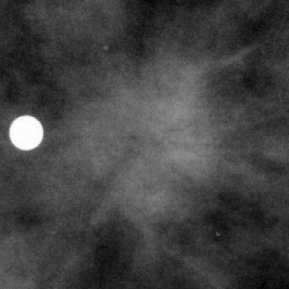
Region of interest cut from a scanned film mammogram (one marked finding); right breast; CC view.
Marked abnormality: calcifications, morphology round and regular / punctate, distribution diffusely scattered; BI-RADS assessment category 2; subtlety rating 1 on a 1 (subtle) to 5 (obvious) scale; pathology result (as recorded, not read from the image): malignant.